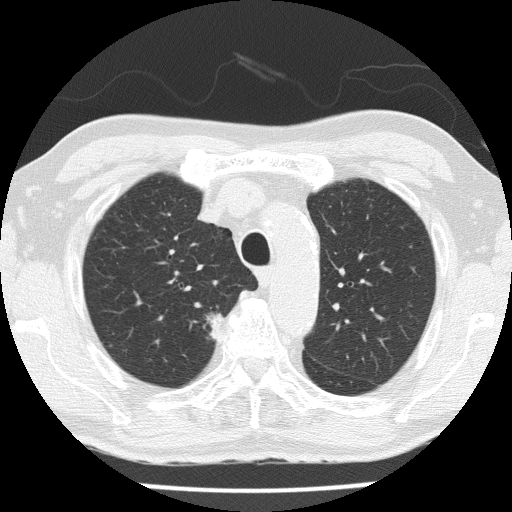
Chest CT (low-dose screening protocol), one axial image, third annual screen, lung window (W 1500 / L -600 HU), 120 kVp, 512 × 512 image matrix, field of view 323 × 323 mm. Male, age 72 years at enrolment. Current smoker at enrolment.
- Lesion marked by an expert reader, bounding box [x1, y1, x2, y2] px = [187, 299, 236, 348].
- The exam's reader record, not a measurement of the box and not confirmed to be the same lesion: non-calcified nodule or mass ≥4 mm, right upper lobe, 14 × 14 mm, spiculated (stellate) margins, soft tissue attenuation, pre-existing on the prior screen: yes; interval growth: yes.